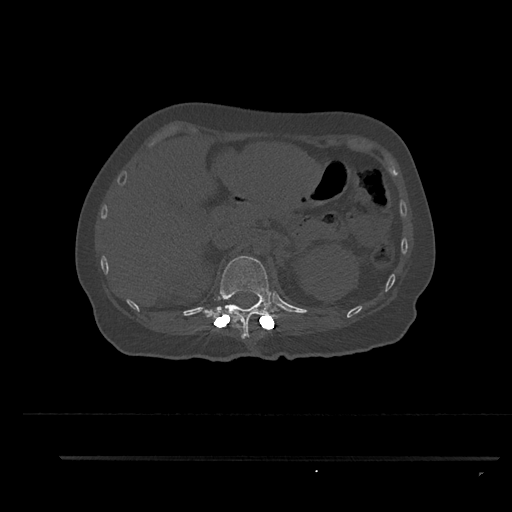
CT including the spine, one axial slice; position 257 of 797 along the scan axis; 120 kVp; bone window (W 1800 / L 400 HU); 0.5 mm slice thickness; 512 × 512 image matrix, field of view 408 × 408 mm. Patient: female, 44 years. Case-level facts recorded for this patient, not image findings: primary cancer: renal; vertebrae with lytic lesions (as recorded): L1.
Structures marked on this image (semi-automatic segmentation, software-assisted and operator-edited):
- T12 vertebra: bounding box [x1, y1, x2, y2] px = [204, 256, 278, 339]